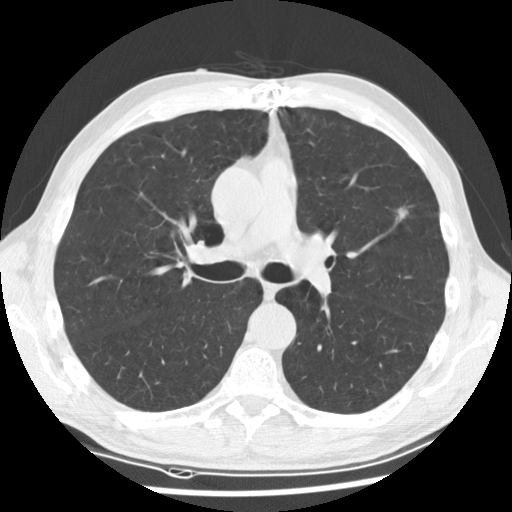
Low-dose screening chest CT, axial slice; baseline annual screen; lung window (W 1500 / L -600 HU); 2.5 mm slice thickness; 512 × 512 image matrix. Male participant, aged 64 years at enrolment.
Expert reader's lesion annotation, bounding box <376,199,427,242> (left, top, right, bottom; pixels). The exam's reader record, not a measurement of the box and not confirmed to be the same lesion: non-calcified nodule or mass ≥4 mm, left upper lobe, 13 × 10 mm, spiculated (stellate) margins, soft tissue attenuation. Official screen result: positive, change unspecified: nodule(s) >= 4 mm or enlarging nodule(s), mass(es), or other non-specific abnormalities suspicious for lung cancer. Participant outcome: lung cancer diagnosed 410 days after this screen — adenocarcinoma, NOS, left upper lobe, poorly differentiated (G3), stage IA (AJCC 6th edition), 10 mm at pathology.